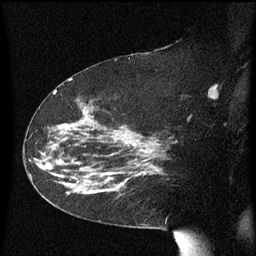
Breast MRI (dynamic contrast-enhanced), one sagittal slice. Position 34 of 60 along the scan axis. Dynamic contrast-enhanced series, image 2 of 3 at this slice position (ordered by acquisition). 1.5 T. TE 4.2 ms, TR 8.4 ms. 2.3 mm slice thickness. 256 × 256 image matrix, field of view 200 × 200 mm. Patient: female, 63 years. From the clinical record (not read from this slice): setting: breast cancer imaged before/during neoadjuvant chemotherapy; receptor status: HER2-positive.
Outlined on this slice (semi-automatic segmentation, software-assisted and operator-edited):
- analysis volume of interest (the breast-tissue region the enhancement analysis was run in; not a lesion): bounding box <71,144,147,199> (left, top, right, bottom; pixels)
- tumour enhancement mask (voxels above the 70 % enhancement threshold inside the analysis volume of interest): <108,150,147,181>